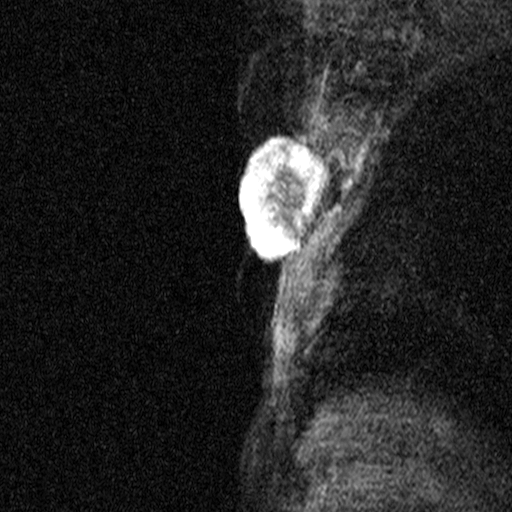
Breast MRI (dynamic contrast-enhanced), one sagittal slice. Dynamic contrast-enhanced study with each time point stored as its own series, time point 2 of 3 at this slice position (early post-contrast, ordered by acquisition time). 1.5 T. TE 4.5 ms, TR 11 ms. 3 mm slice thickness. 512 × 512 image matrix. Patient: female, 44 years. From the clinical record (not read from this slice): setting: breast cancer imaged before/during neoadjuvant chemotherapy; receptor status: HR-positive, HER2-negative.
Outlined on this slice (semi-automatically segmented with operator editing):
- analysis volume of interest (the breast-tissue region the enhancement analysis was run in; not a lesion): bounding box [x1, y1, x2, y2] px = [218, 118, 327, 291]
- tumour enhancement mask (voxels above the 90 % enhancement threshold inside the analysis volume of interest): [239, 135, 327, 257]